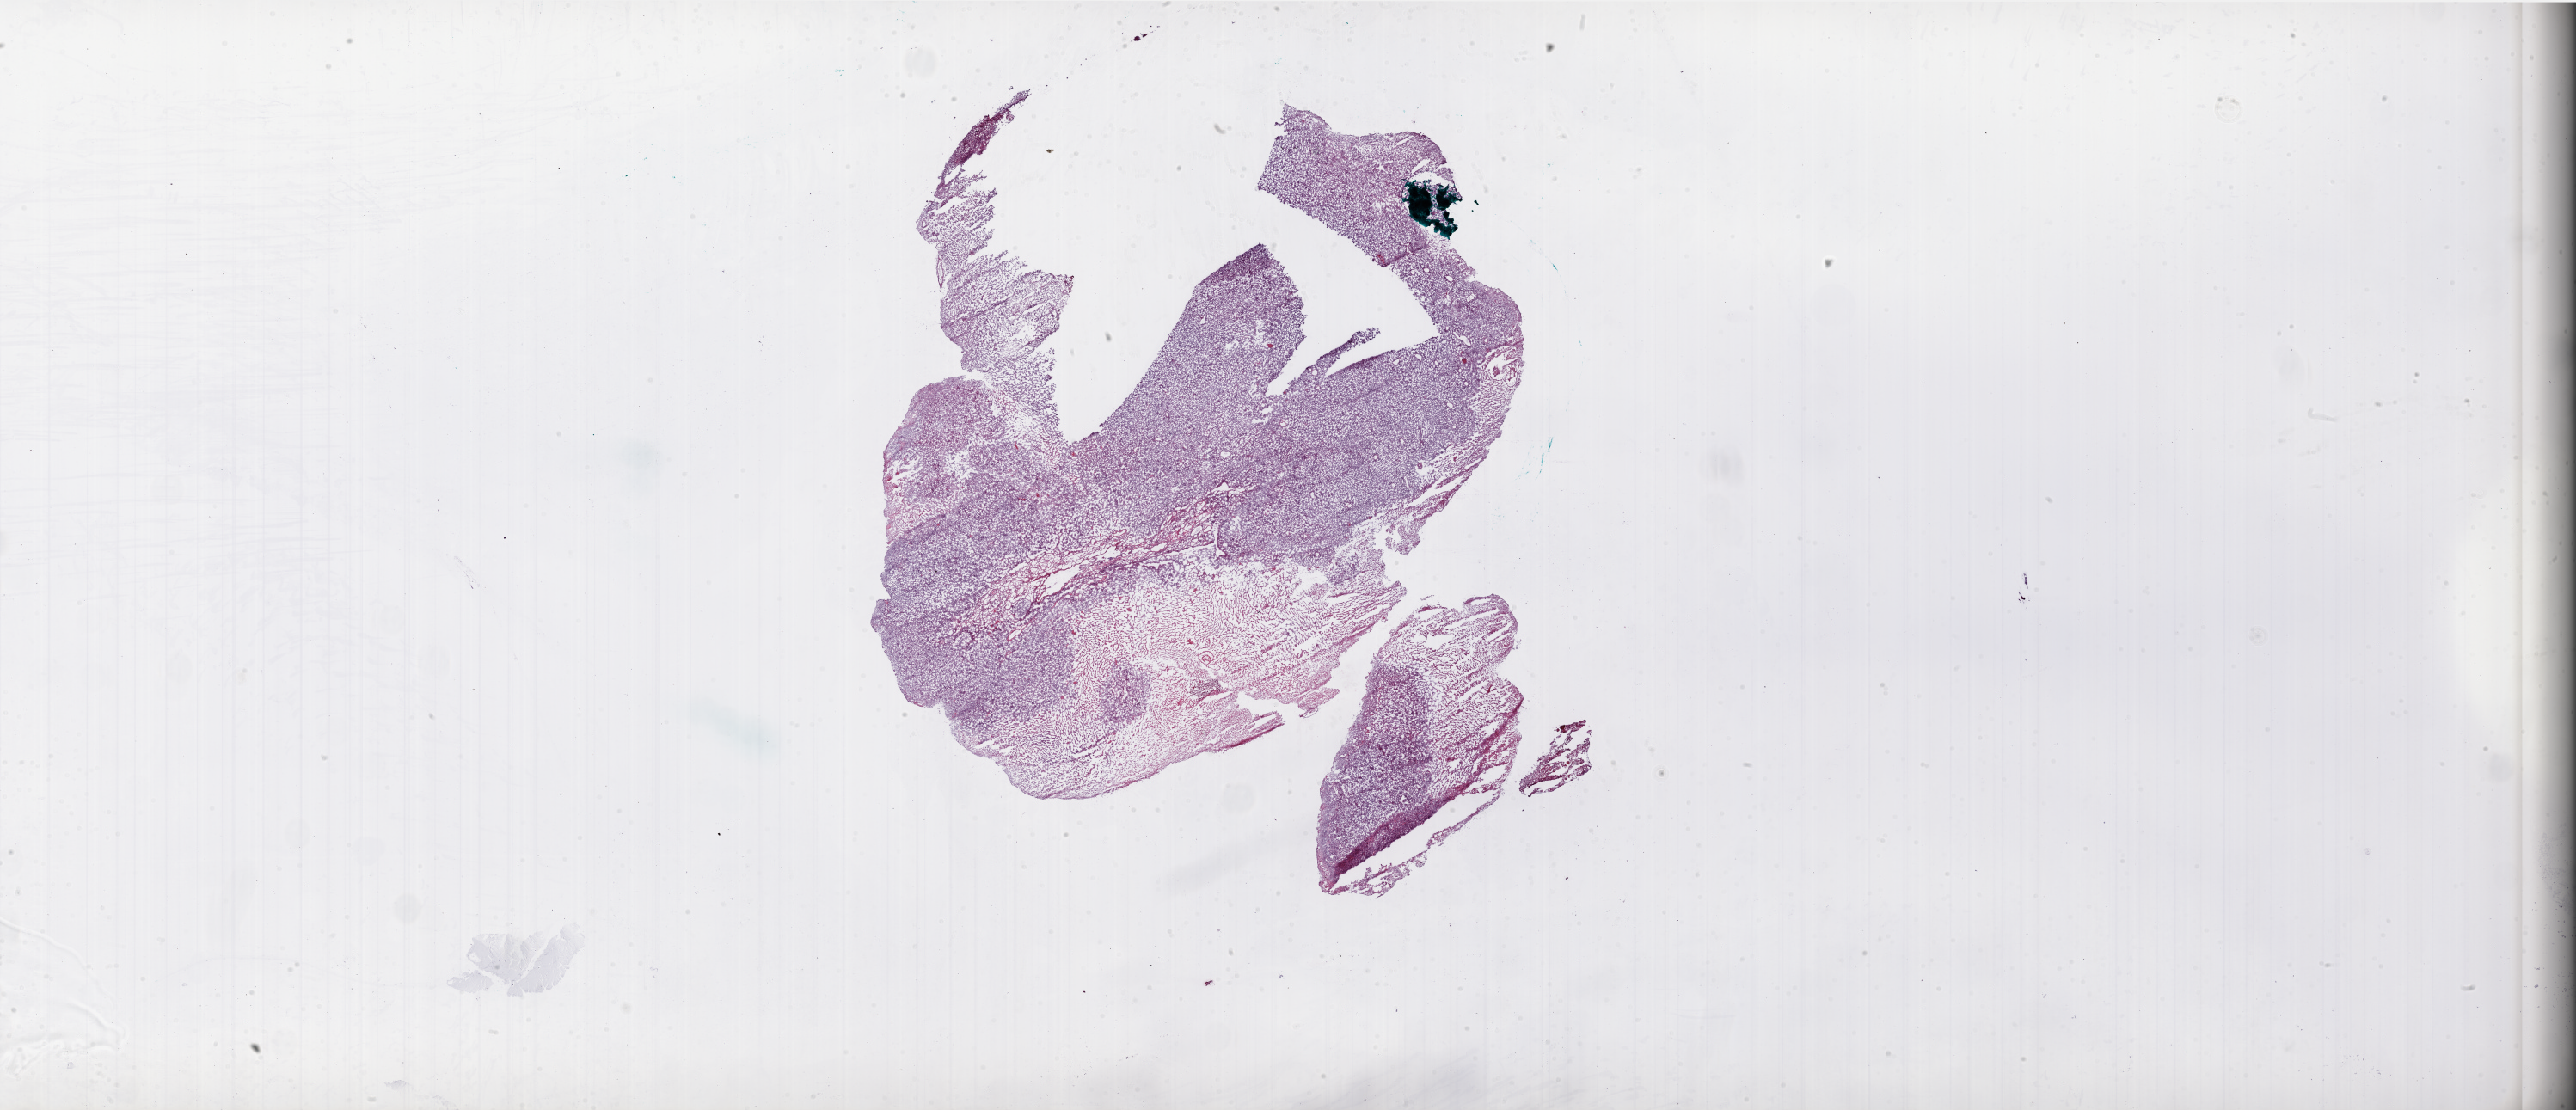
Whole-slide histology image, H&E-stained, a low-resolution overview of the entire scanned area, about 48.0 x 20.7 mm (acquisition: 20x scan). Frozen section from the bottom of the tissue portion. Primary tumour sample from the brain. Patient: female, age at initial diagnosis 77 years. Pathologist review of this section (percent, as recorded): tumour cells 60%, tumour nuclei 100%, normal cells 0%, stromal cells 0%, necrosis 40%. Inflammatory infiltration, as recorded: lymphocyte infiltration 0%.
Pathologic diagnosis: Glioblastoma.